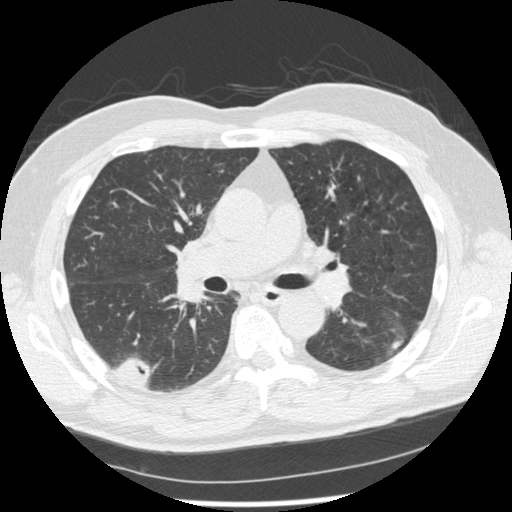
Chest CT (low-dose screening protocol), one axial image. Second annual screen. Lung window (W 1500 / L -600 HU). 1.25 mm slice thickness. Standard (soft-tissue) reconstruction kernel (STANDARD). Slice 106 of 227 in the series. Male participant, aged 74 years at enrolment.
Expert-annotated lung lesion, bounding box [x1, y1, x2, y2] px = [372, 317, 420, 369]. The screening reader recorded 7 non-calcified nodules or masses ≥4 mm on this exam (right upper lobe, right lower lobe, right upper lobe, right lower lobe, left lower lobe, left upper lobe, left upper lobe); which of them this box marks is not recorded. Official screen result: positive, other. Later outcome: lung cancer diagnosed 43 days after this screen — squamous cell carcinoma, NOS, left lower lobe, well differentiated (G1), stage IA (AJCC 6th edition), 28 mm at pathology.